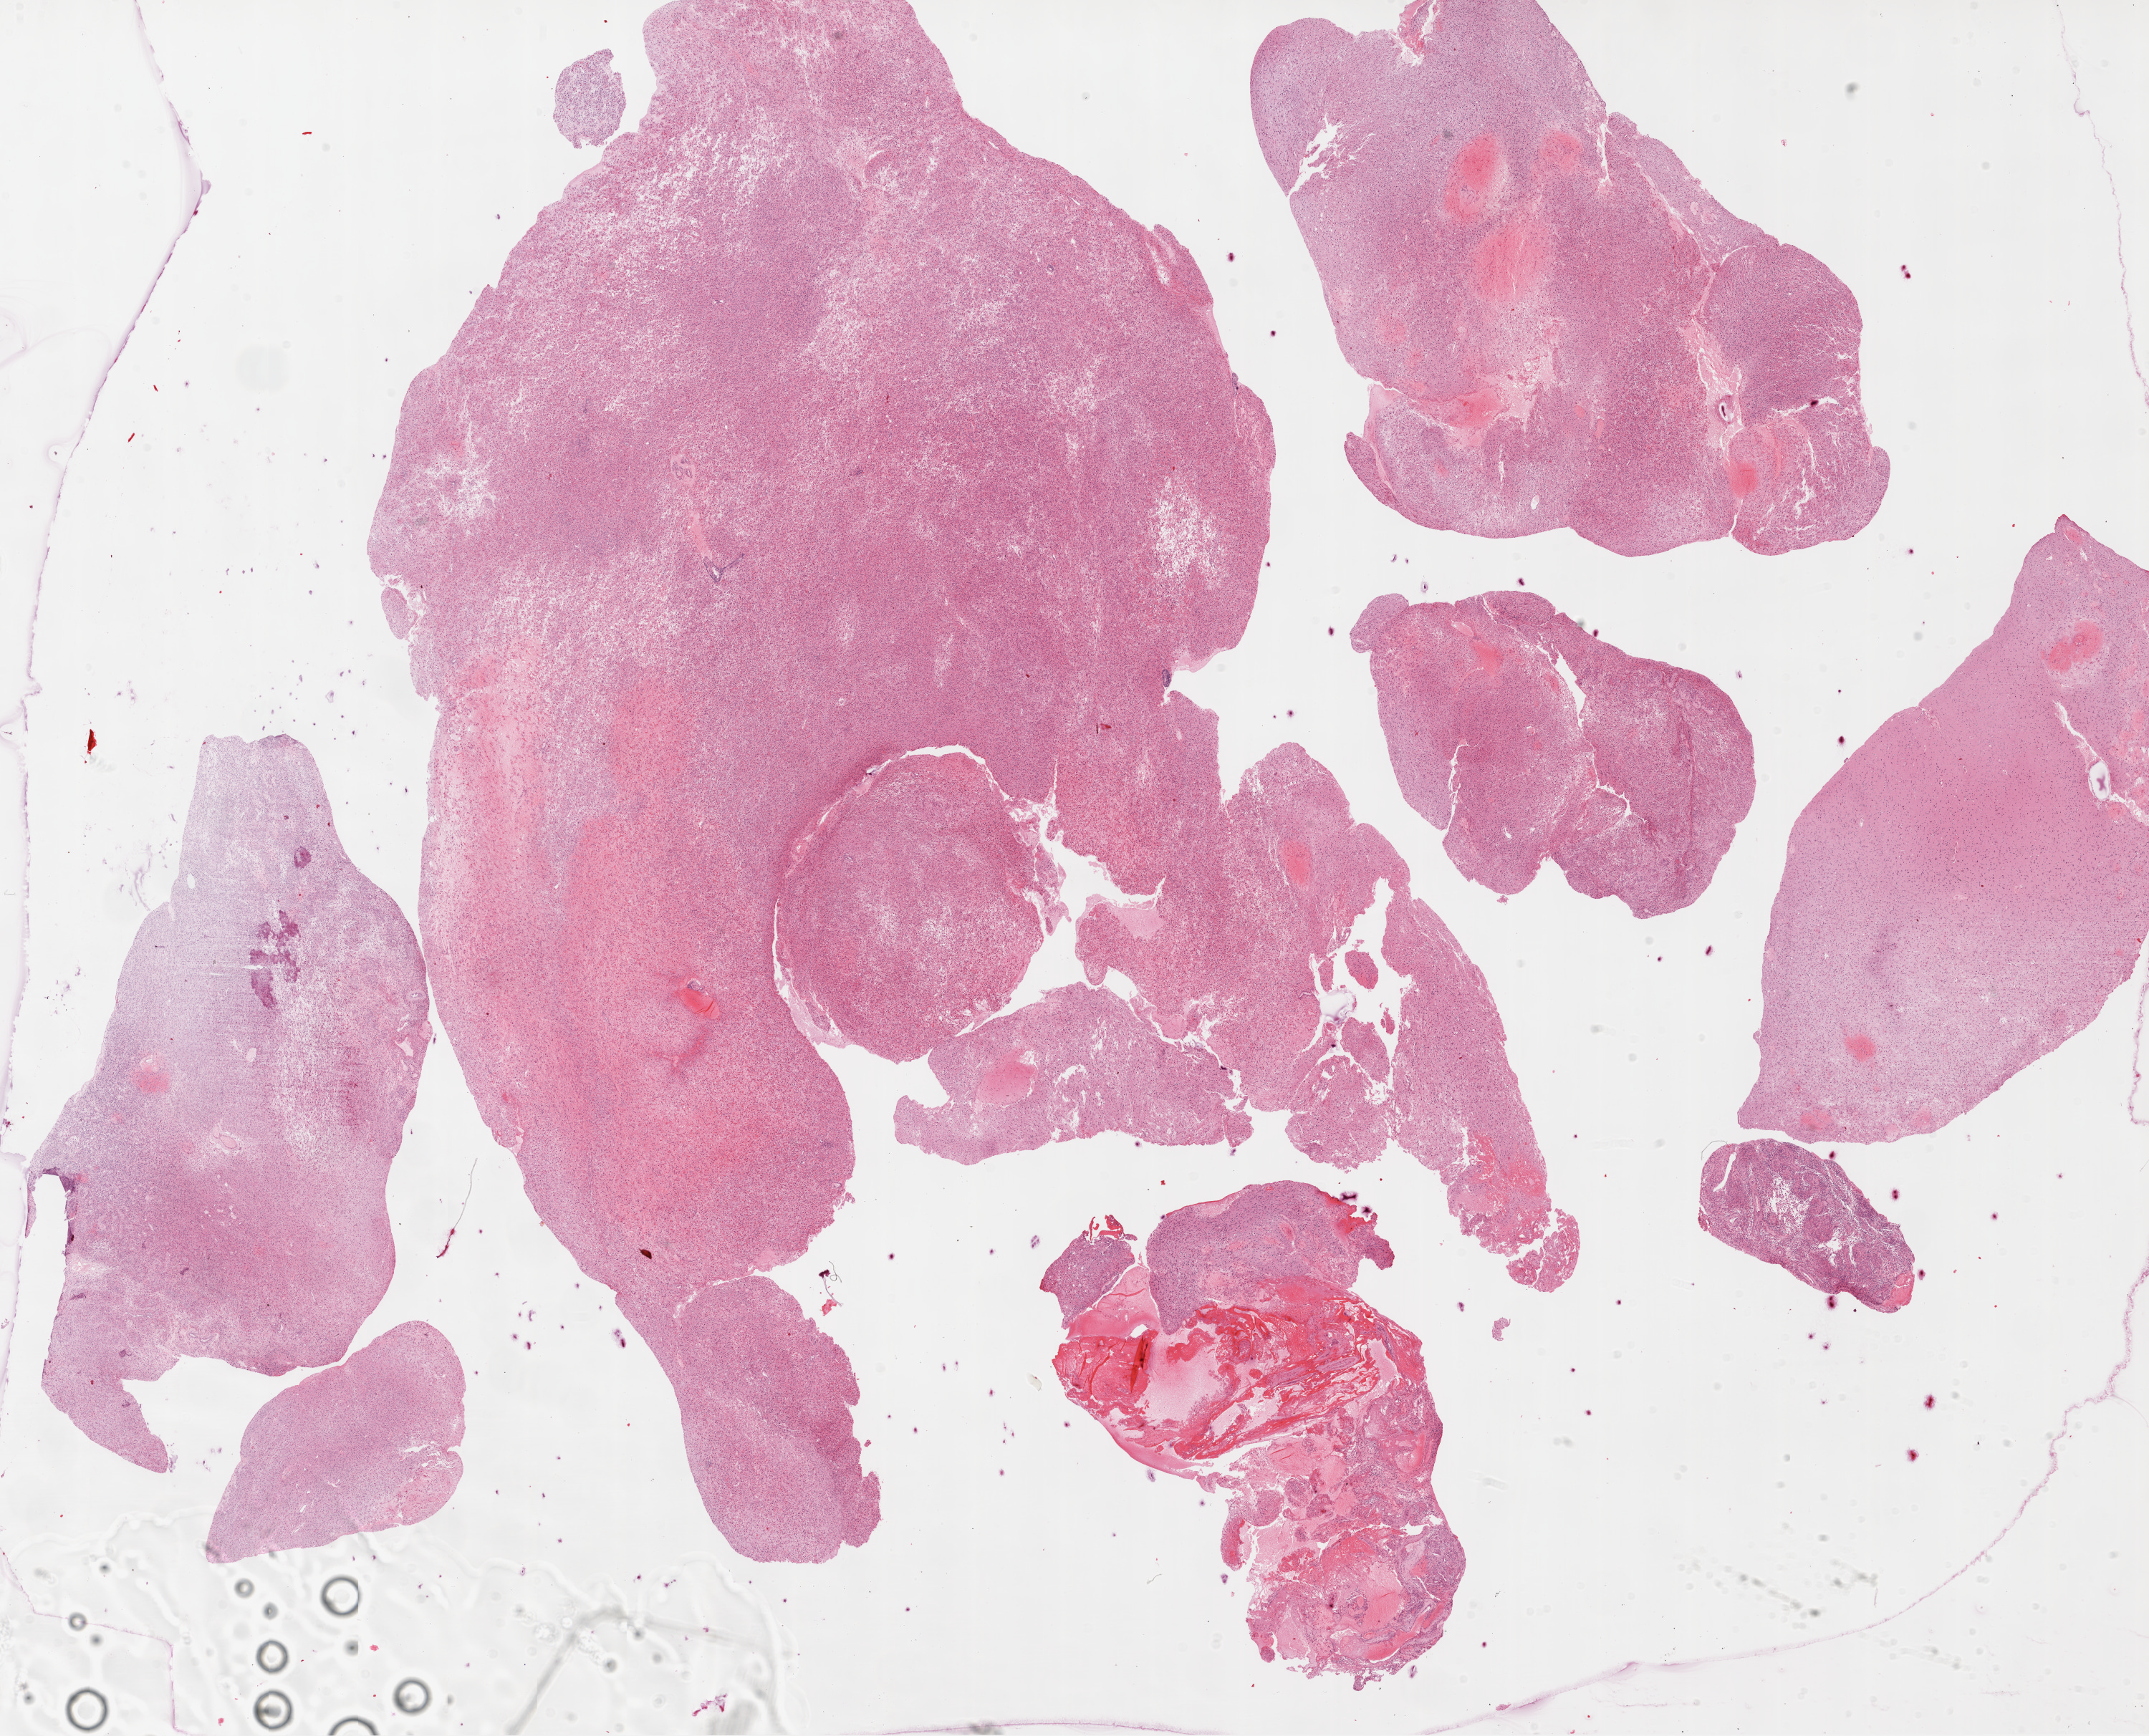
Whole-slide histology image, H&E-stained, whole scanned area (about 24.1 x 19.5 mm, acquisition: 20x scan) shown as a low-resolution overview. FFPE section. Brain, primary tumour sample. Patient: male, age at initial diagnosis 56 years.
Diagnosis: Glioblastoma.